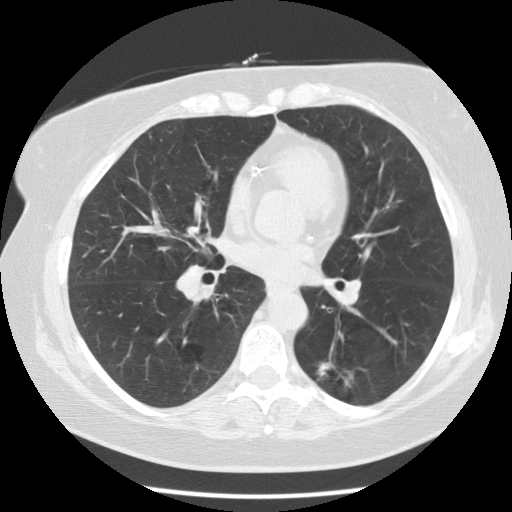
Low-dose screening chest CT, axial slice, second annual screen, lung window (W 1500 / L -600 HU), standard (soft-tissue) reconstruction kernel (STANDARD). Female participant, aged 59 years at enrolment. Current smoker at enrolment.
- Expert-annotated lung lesion, bounding box [x1, y1, x2, y2] px = [296, 343, 372, 410].
- The screening reader recorded 5 non-calcified nodules or masses ≥4 mm on this exam; which of them this box marks is not recorded.
- Official screen result: positive, other.